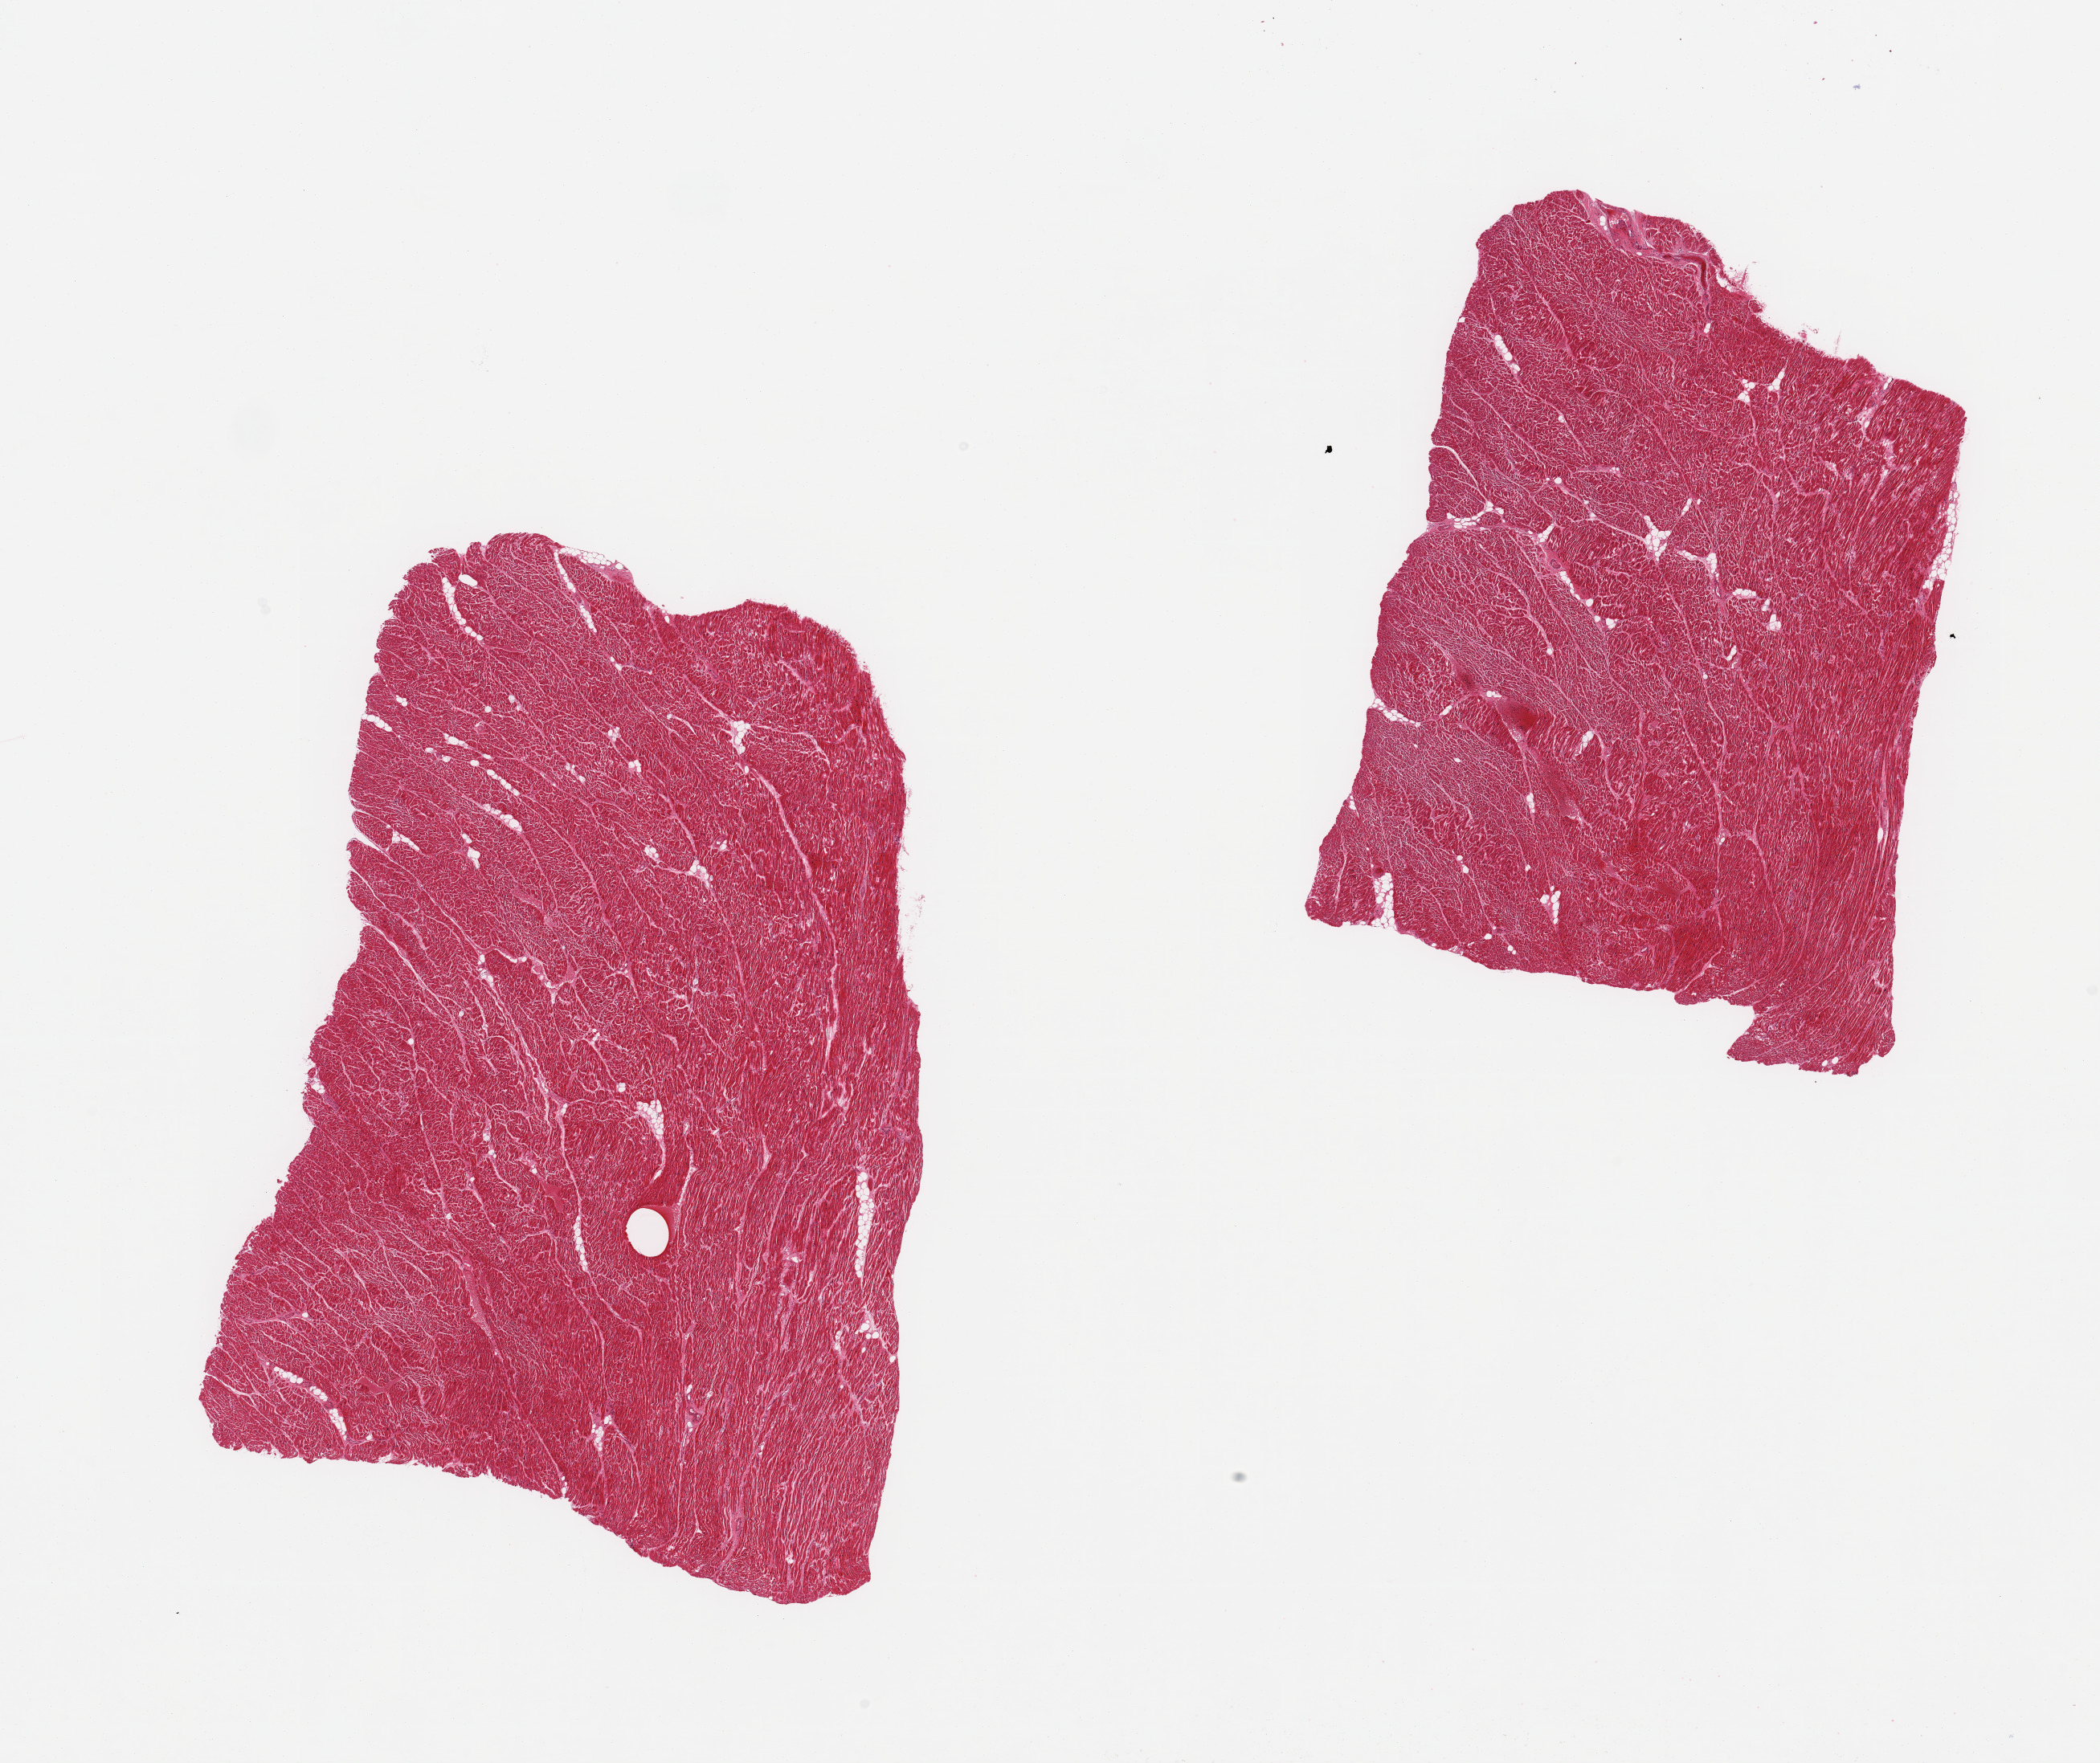
Hematoxylin and eosin (H&E) whole-slide image, brightfield — low-resolution overview of the scanned area, about 20.7 x 17.4 mm; PAXgene-fixed, paraffin-embedded tissue; target tissue: heart; donor tissue sample.
Review note (as recorded): 2 pieces, moderate interstitial fibrosis/chronic ischemic change.